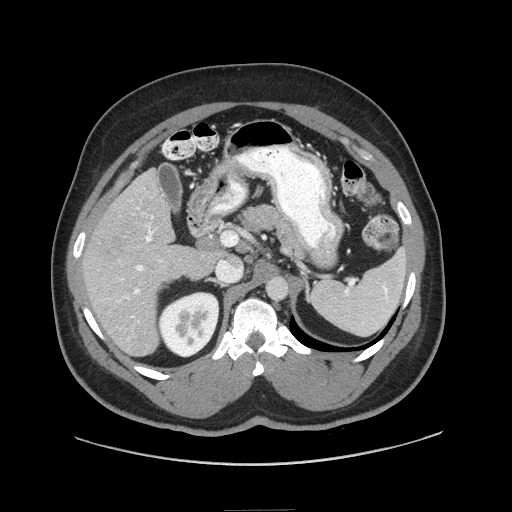
Contrast-enhanced abdominal CT (liver protocol), one axial slice; slice 42 of 87 in the series (ordered by position); soft-tissue window (W 400 / L 40 HU); 512 × 512 image matrix, field of view 440 × 440 mm. Case-level facts recorded for this patient, not image findings: diagnosis: hepatocellular carcinoma (patient treated with transarterial chemoembolisation; whether this scan precedes or follows treatment is not stated here); TNM stage (as recorded): Stage-II; Child-Pugh class: A; tumour differentiation: moderately differentiated.
Annotated regions visible in this slice (semi-automatic segmentation, software-assisted and operator-edited):
- liver parenchyma outside the tumour (the mass and vessels are separate outlines, so this box may not span the whole liver): bounding box [x1, y1, x2, y2] px = [82, 168, 220, 356]
- liver vessels: [104, 207, 162, 323]